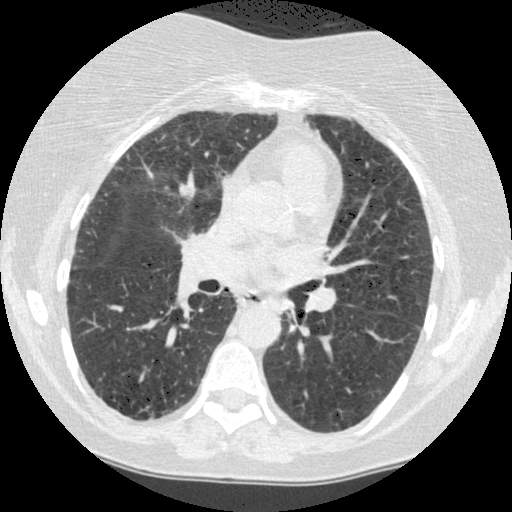
Chest CT (low-dose screening protocol), one axial image; baseline screening round; lung window (W 1500 / L -600 HU); standard (soft-tissue) reconstruction kernel (STANDARD); slice 205 of 442 in the series; 512 × 512 image matrix. Female, age 60 years at enrolment. Former smoker at enrolment.
Lesion marked by an expert reader, bounding box <268,292,309,333> (left, top, right, bottom; pixels). The screening reader recorded 2 non-calcified nodules or masses ≥4 mm on this exam; which of them this box marks is not recorded. Later outcome: lung cancer diagnosed 794 days after this screen (after the third annual screen) — small cell carcinoma, NOS, left lower lobe, undifferentiated (G4), stage IV (AJCC 6th edition), 69 mm at pathology.